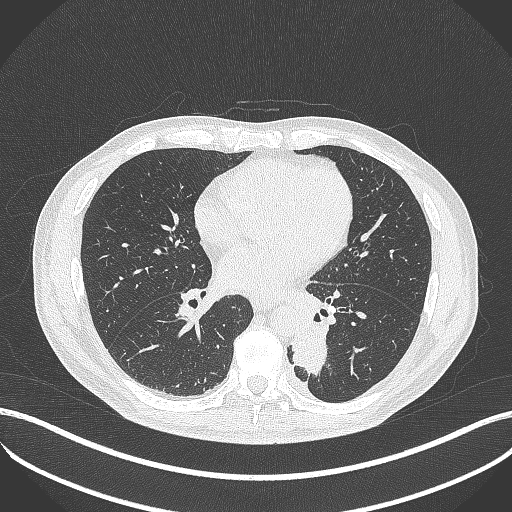
Chest CT, one axial slice. Slice 180 of 451 in the series (ordered by position). 120 kVp. Lung window (W 1500 / L -600 HU). 512 × 512 image matrix. Male patient, age 72 years. From the clinical record (not read from this slice): clinical TNM (as recorded): T2b N0 M1.
Annotated regions visible in this slice (bounding box drawn by a radiologist):
- lung tumour (recorded histology: adenocarcinoma): bounding box <285,317,333,379> (left, top, right, bottom; pixels)